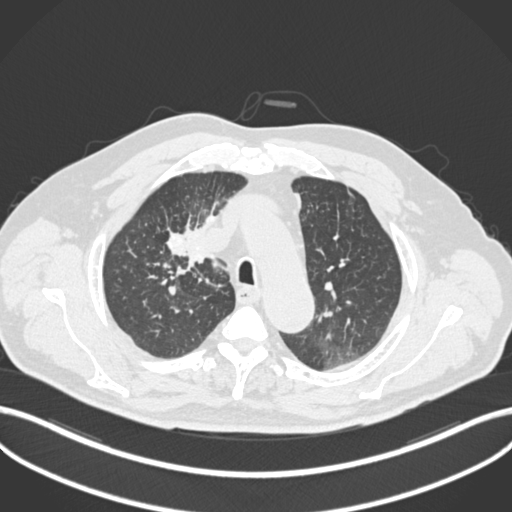
Chest CT, one axial slice. Position 152 of 255 along the scan axis. Reconstruction kernel B30f. Lung window (W 1500 / L -600 HU). 1 mm slice thickness. 512 × 512 image matrix, field of view 400 × 400 mm. Patient: male, 60 years. From the clinical record (not read from this slice): clinical TNM (as recorded): T1b N1 M0.
Annotated regions visible in this slice (bounding box drawn by a radiologist):
- lung tumour (recorded histology: squamous cell carcinoma): box from (x=164, y=220) to (x=212, y=268) px